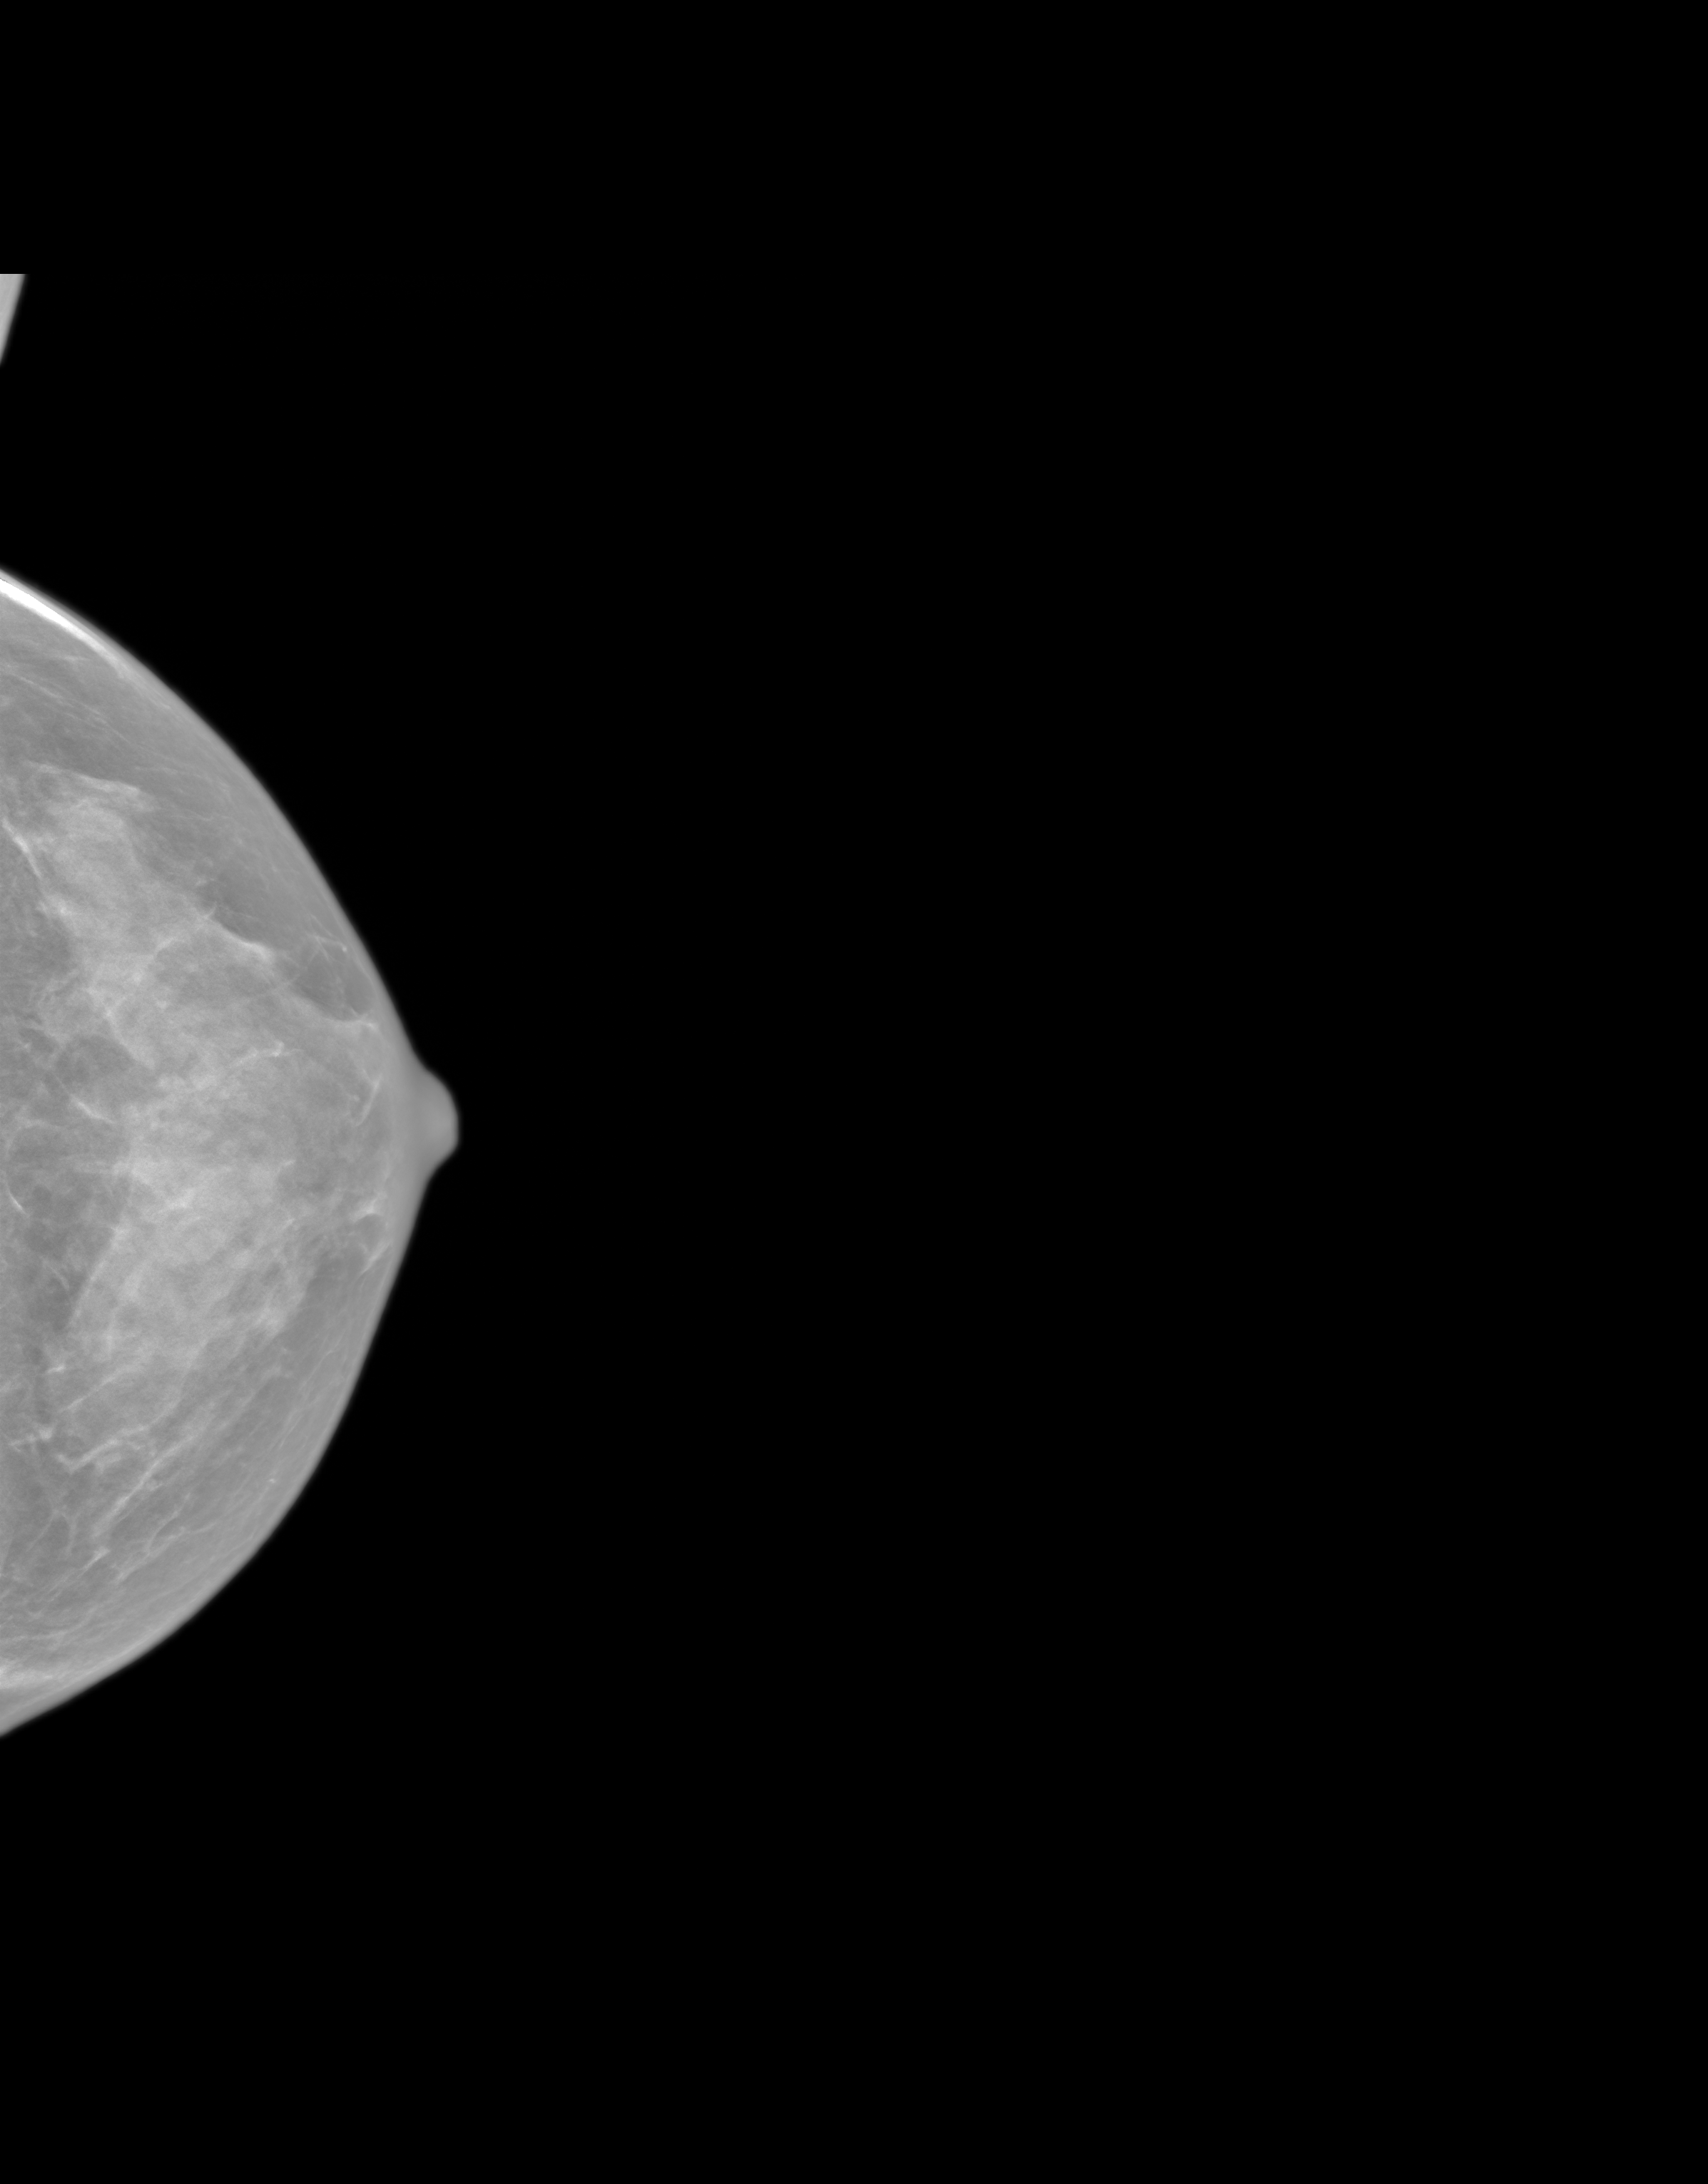
Annual screening mammography examination, system: SenoIris_1SP2(440). Patient aged 56 years (female).
Image type: synthesized 2-D view from tomosynthesis. Breast: left. Projection: cranio-caudal projection.